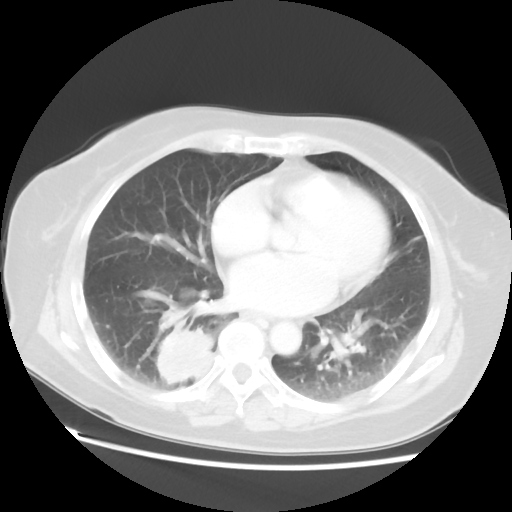
Chest CT, one axial slice. Slice 25 of 52 in the series (ordered by position). 120 kVp. Lung window (W 1500 / L -600 HU). 512 × 512 image matrix, field of view 356 × 356 mm. Patient: female, 69 years. Case-level facts recorded for this patient, not image findings: clinical TNM (as recorded): T2 N1 M1a.
Structures marked on this image (rectangle marked by the reading radiologist):
- lung tumour (recorded histology: adenocarcinoma): box from (x=155, y=324) to (x=213, y=388) px